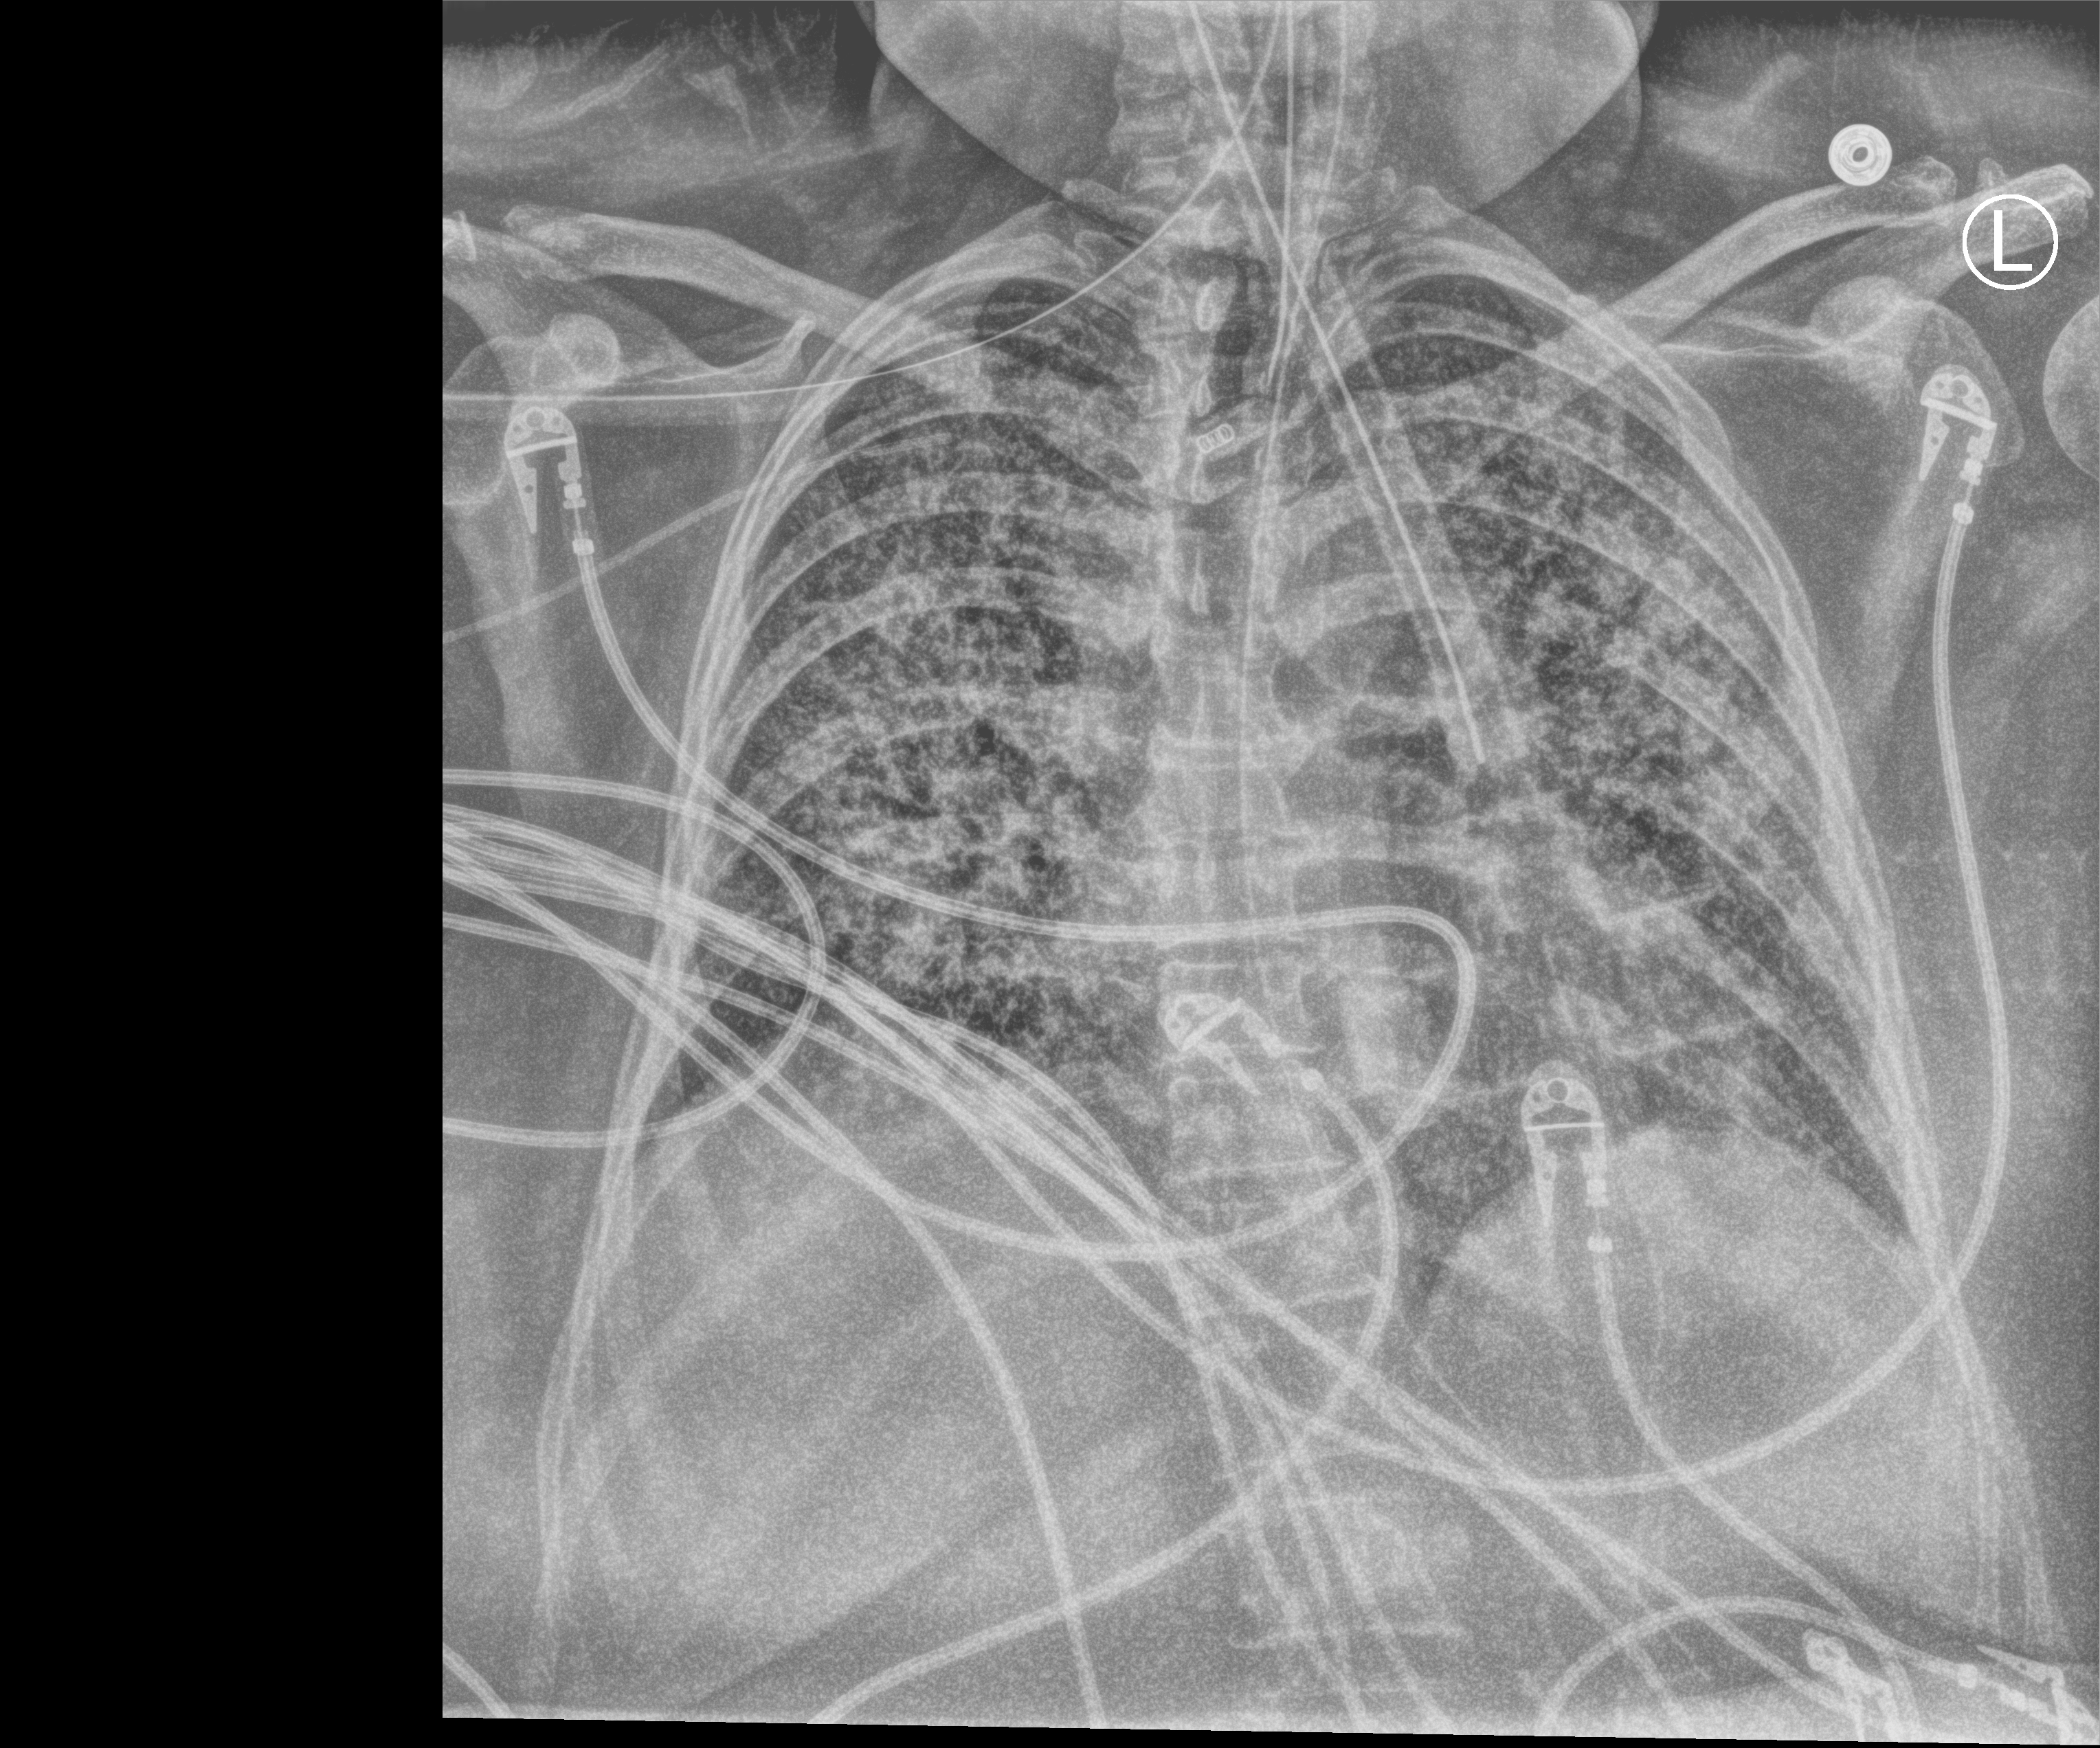
Portable chest radiograph. Patient hospitalised with COVID-19; female, aged 18–59 years.
From the hospital-stay record, not from the radiograph (when in the stay this image was taken is not recorded): hypertension (admission record): yes; mechanically ventilated during this hospital stay: yes.